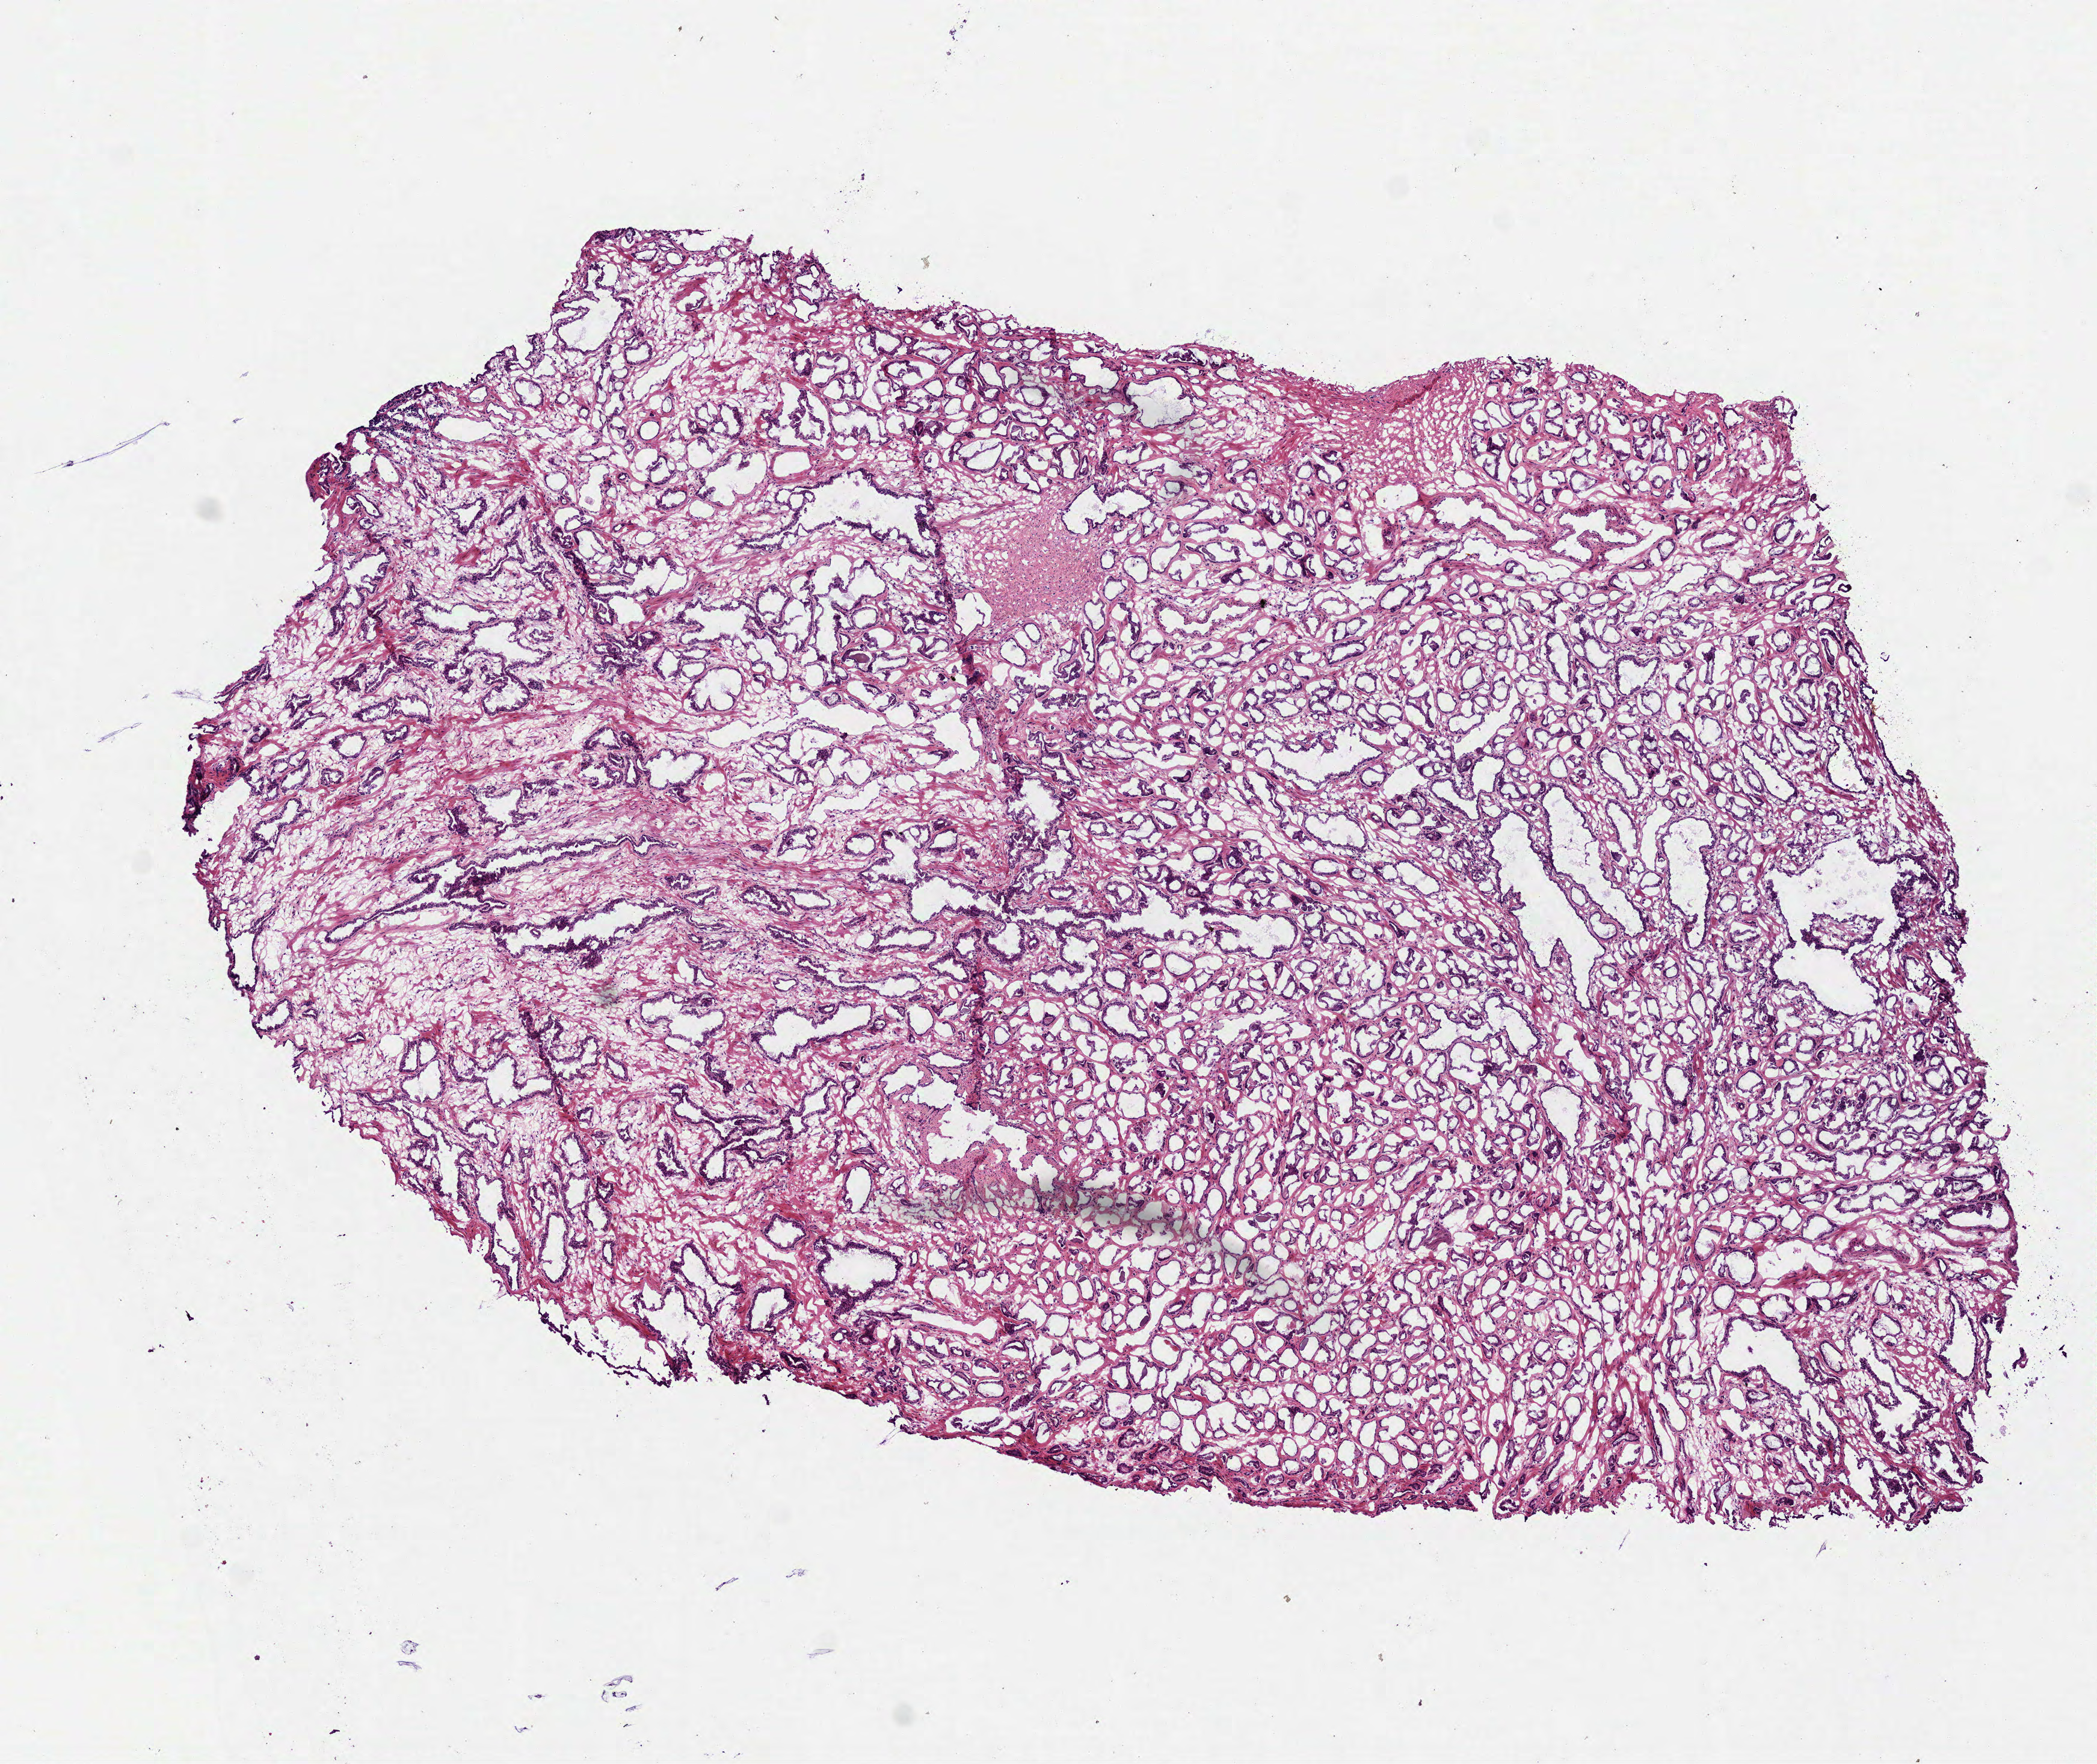
Whole-slide histology image, H&E-stained, low-resolution overview of the scanned area, about 7.0 x 5.9 mm (from a 40x scan). Frozen section. Sample: primary tumour, prostate. Patient: male, age at initial diagnosis 51 years. Gleason score: 7 (3+4). Slide review estimates, as recorded: tumour cells 60%, tumour nuclei 60%, normal cells 25%, stromal cells 13%, necrosis 0%. Inflammatory infiltration, as recorded: lymphocyte infiltration 2%, monocyte infiltration 0%, neutrophil infiltration 0%.
• pathologic diagnosis: Acinar cell carcinoma (prostate gland)
• laterality: bilateral